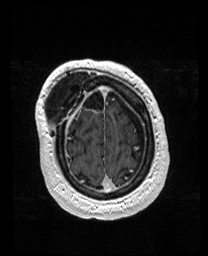
Brain MRI from a brain-tumour surgery series, one axial slice. T1-weighted post-contrast. 1 mm slice thickness. 208 × 256 image matrix, field of view 208 × 256 mm. Case-level facts recorded for this patient, not image findings: histopathology: Astrocytoma; WHO grade: 4; IDH mutation: yes.
Outlined on this slice (outlined manually by an expert reader):
- previous resection cavity: bounding box [x1, y1, x2, y2] px = [56, 87, 106, 108]